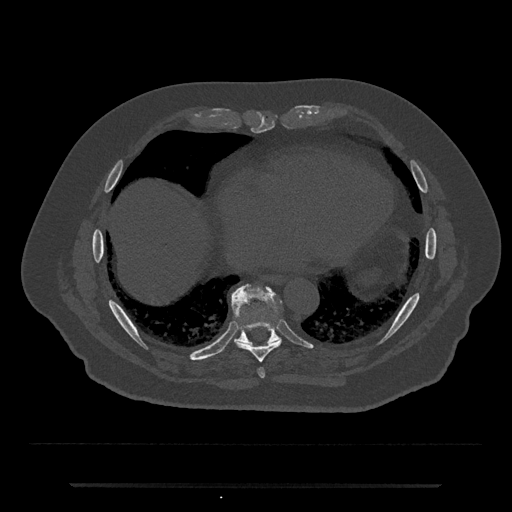
CT including the spine, one axial slice; position 789 of 797 along the scan axis; reconstruction kernel Br40s/3; bone window (W 1800 / L 400 HU); 512 × 512 image matrix. Male patient, age 80 years. From the clinical record (not read from this slice): primary cancer: prostate; vertebrae with lytic lesions (as recorded): L1, T11.
Structures marked on this image (semi-automatically segmented with operator editing):
- T8 vertebra: bounding box <236,321,281,363> (left, top, right, bottom; pixels)
- T9 vertebra: <232,284,282,348>